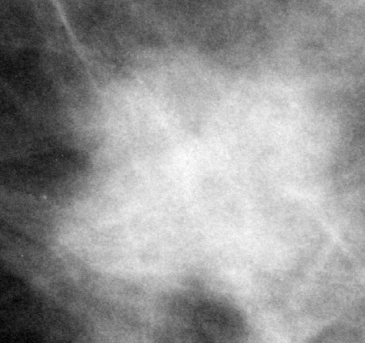
Cropped region of a digitized screen-film mammogram centred on a radiologist-marked abnormality, right breast, CC view.
- Mass, shape lobulated, margins circumscribed; BI-RADS assessment category 4; subtlety rating 5 on a 1 (subtle) to 5 (obvious) scale; pathology (as recorded): benign.